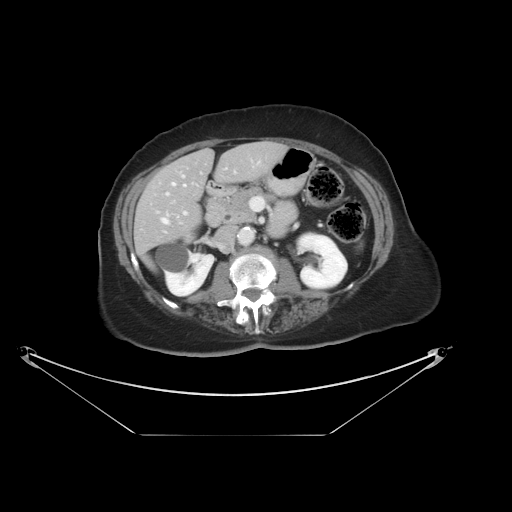
Contrast-enhanced abdominal CT, one axial slice; intravenous contrast given; soft-tissue window (W 400 / L 40 HU); 512 × 512 image matrix, field of view 500 × 500 mm. Female patient, age 70 years. From the clinical record (not read from this slice): diagnosis: colorectal cancer liver metastases, imaged before liver resection; multiple liver metastases: no; largest metastasis: 2.5 cm; disease in both lobes: no.
Outlined on this slice (expert manual segmentation):
- hepatic veins: bounding box <162,182,186,224> (left, top, right, bottom; pixels)
- liver: <136,142,285,254>
- planned liver remnant (the part of the liver to remain after resection): <136,142,285,254>
- portal vein (with intrahepatic branches): <166,172,236,215>